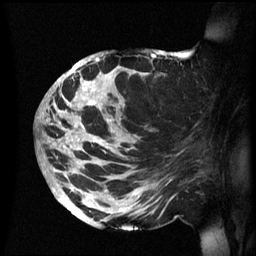
Breast MRI (dynamic contrast-enhanced), one sagittal slice; slice 33 of 60 in the series (ordered by position); dynamic contrast-enhanced series, image 2 of 3 at this slice position (ordered by acquisition); 1.5 T; TE 4.2 ms, TR 8.4 ms; 256 × 256 image matrix. Female patient, age 48 years.
Structures marked on this image (semi-automatic segmentation, software-assisted and operator-edited):
- analysis volume of interest (the breast-tissue region the enhancement analysis was run in; not a lesion): bounding box [x1, y1, x2, y2] px = [42, 49, 194, 231]
- tumour enhancement mask (voxels above the 70 % enhancement threshold inside the analysis volume of interest): [42, 52, 176, 217]